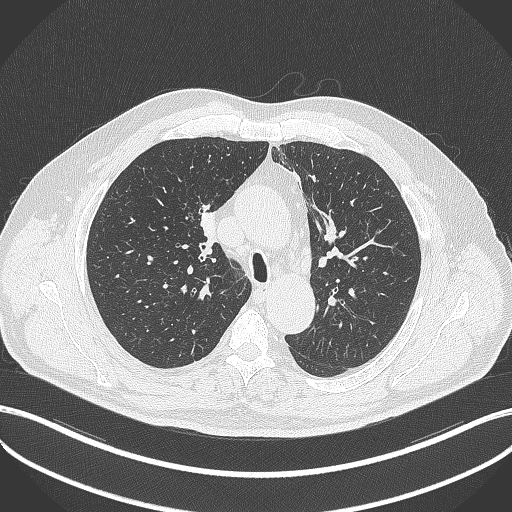
Chest CT, one axial slice. Position 265 of 411 along the scan axis. Reconstruction kernel B70f. 120 kVp. Lung window (W 1500 / L -600 HU). 1 mm slice thickness. 512 × 512 image matrix, field of view 400 × 400 mm. Male patient, age 60 years. From the clinical record (not read from this slice): clinical TNM (as recorded): T1b N1 M0.
Annotated regions visible in this slice (bounding box drawn by a radiologist):
- lung tumour (recorded histology: squamous cell carcinoma): bounding box (x1, y1, x2, y2) in pixels: (190, 206, 223, 253)